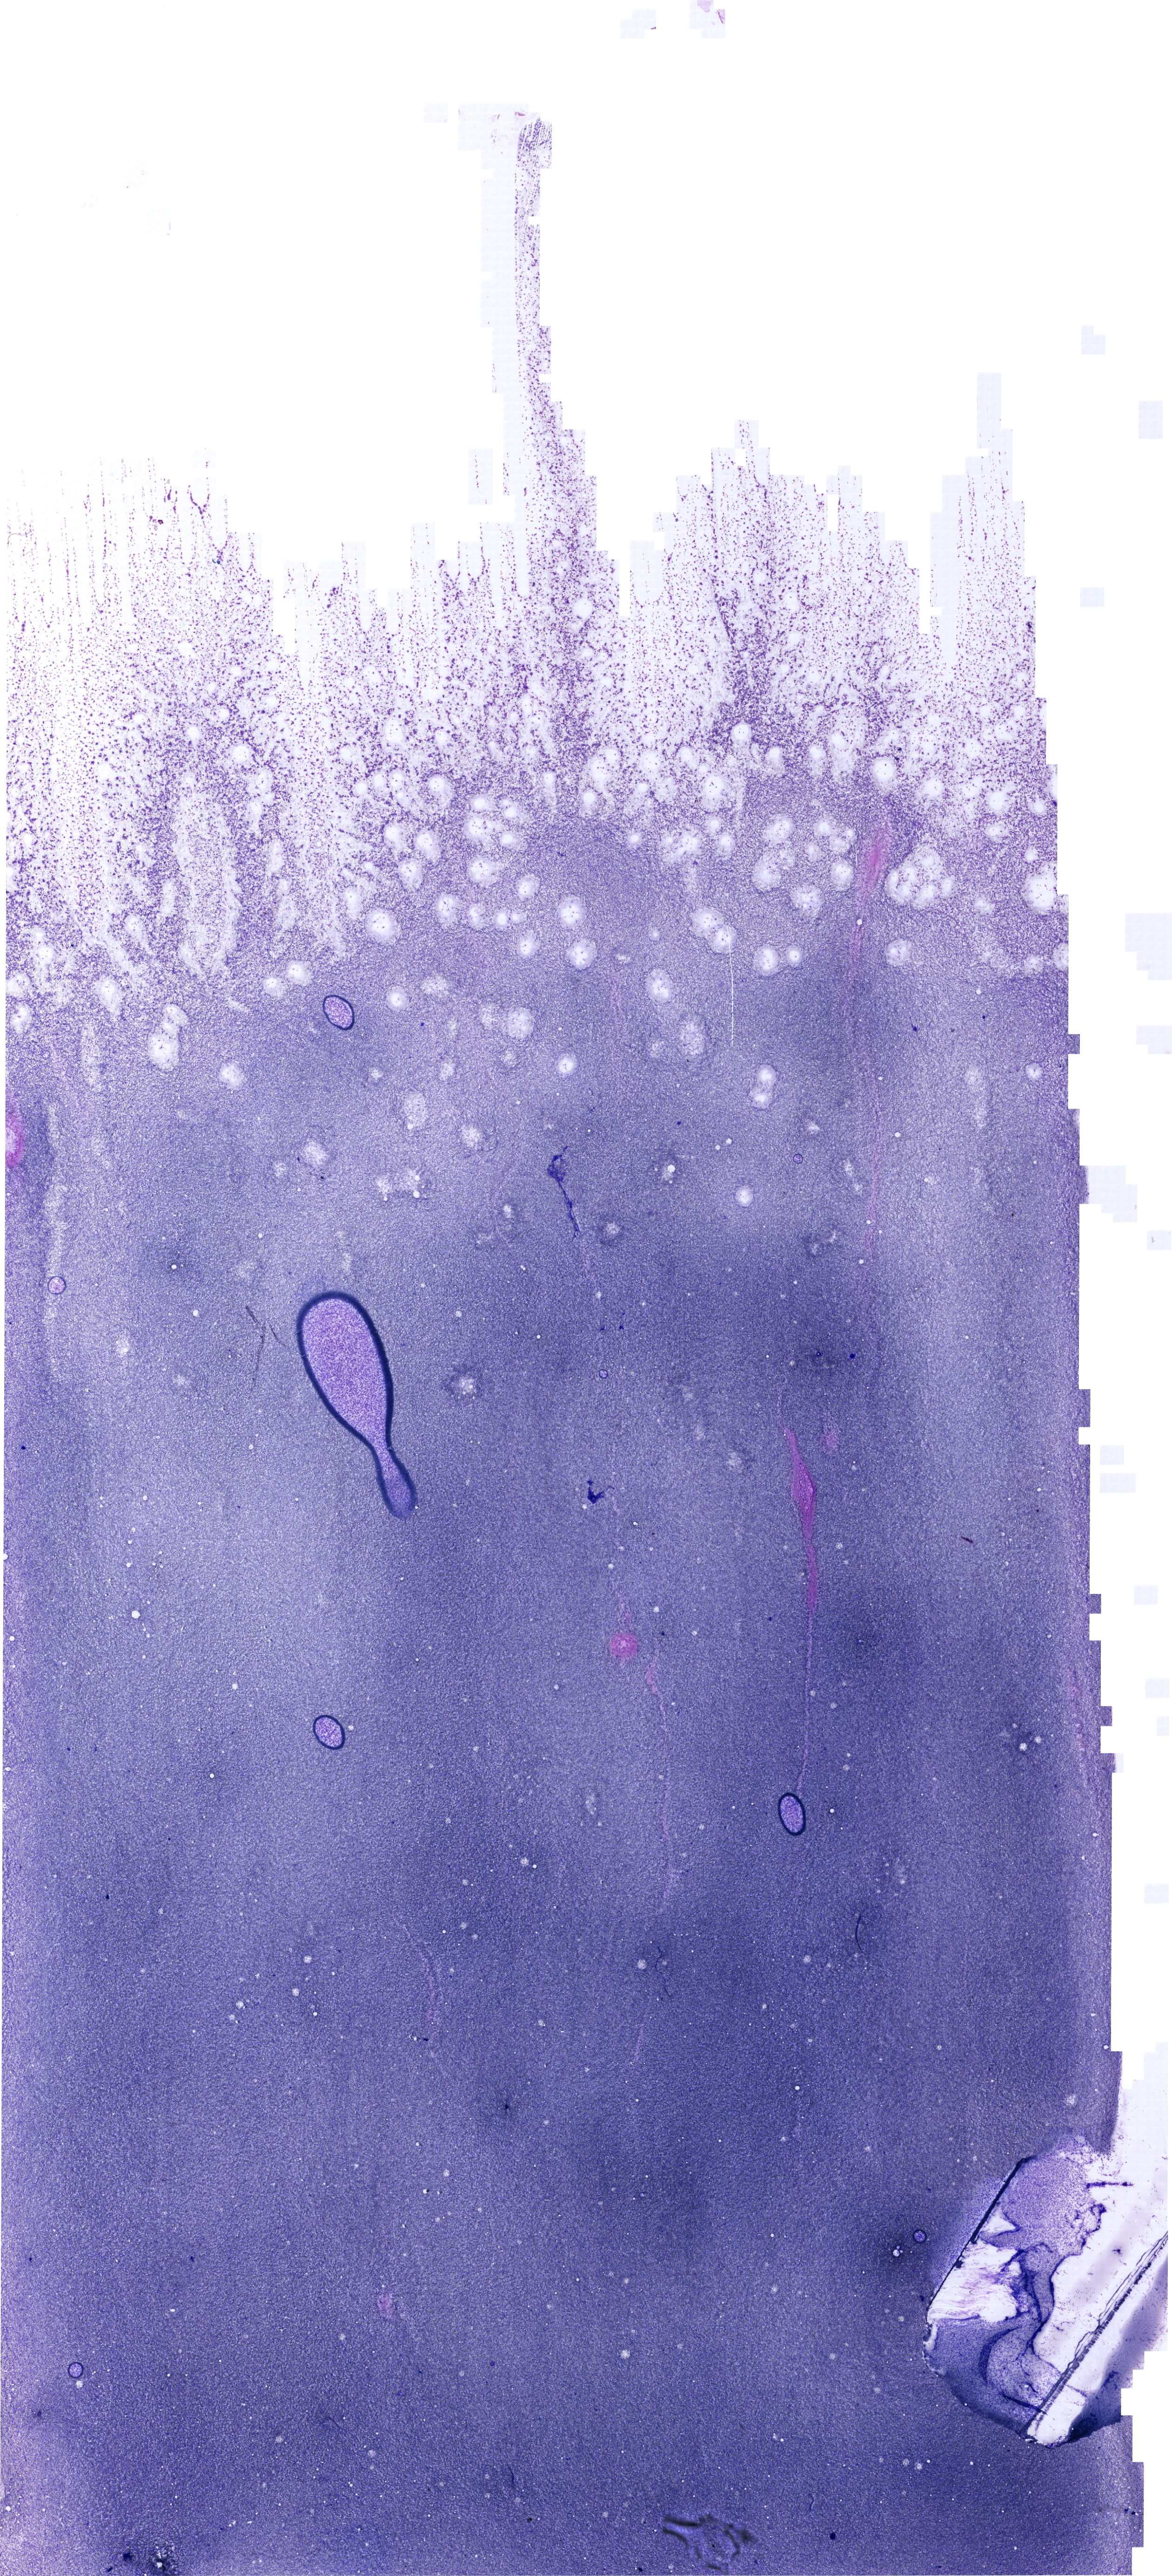
May-Grünwald–Giemsa-stained marrow aspirate smear (whole slide), a low-resolution overview of the entire scanned area, about 19.7 x 43.2 mm. Patient sex: female.
• diagnosis: Mixed Phenotype Acute Leukemia, B/Myeloid